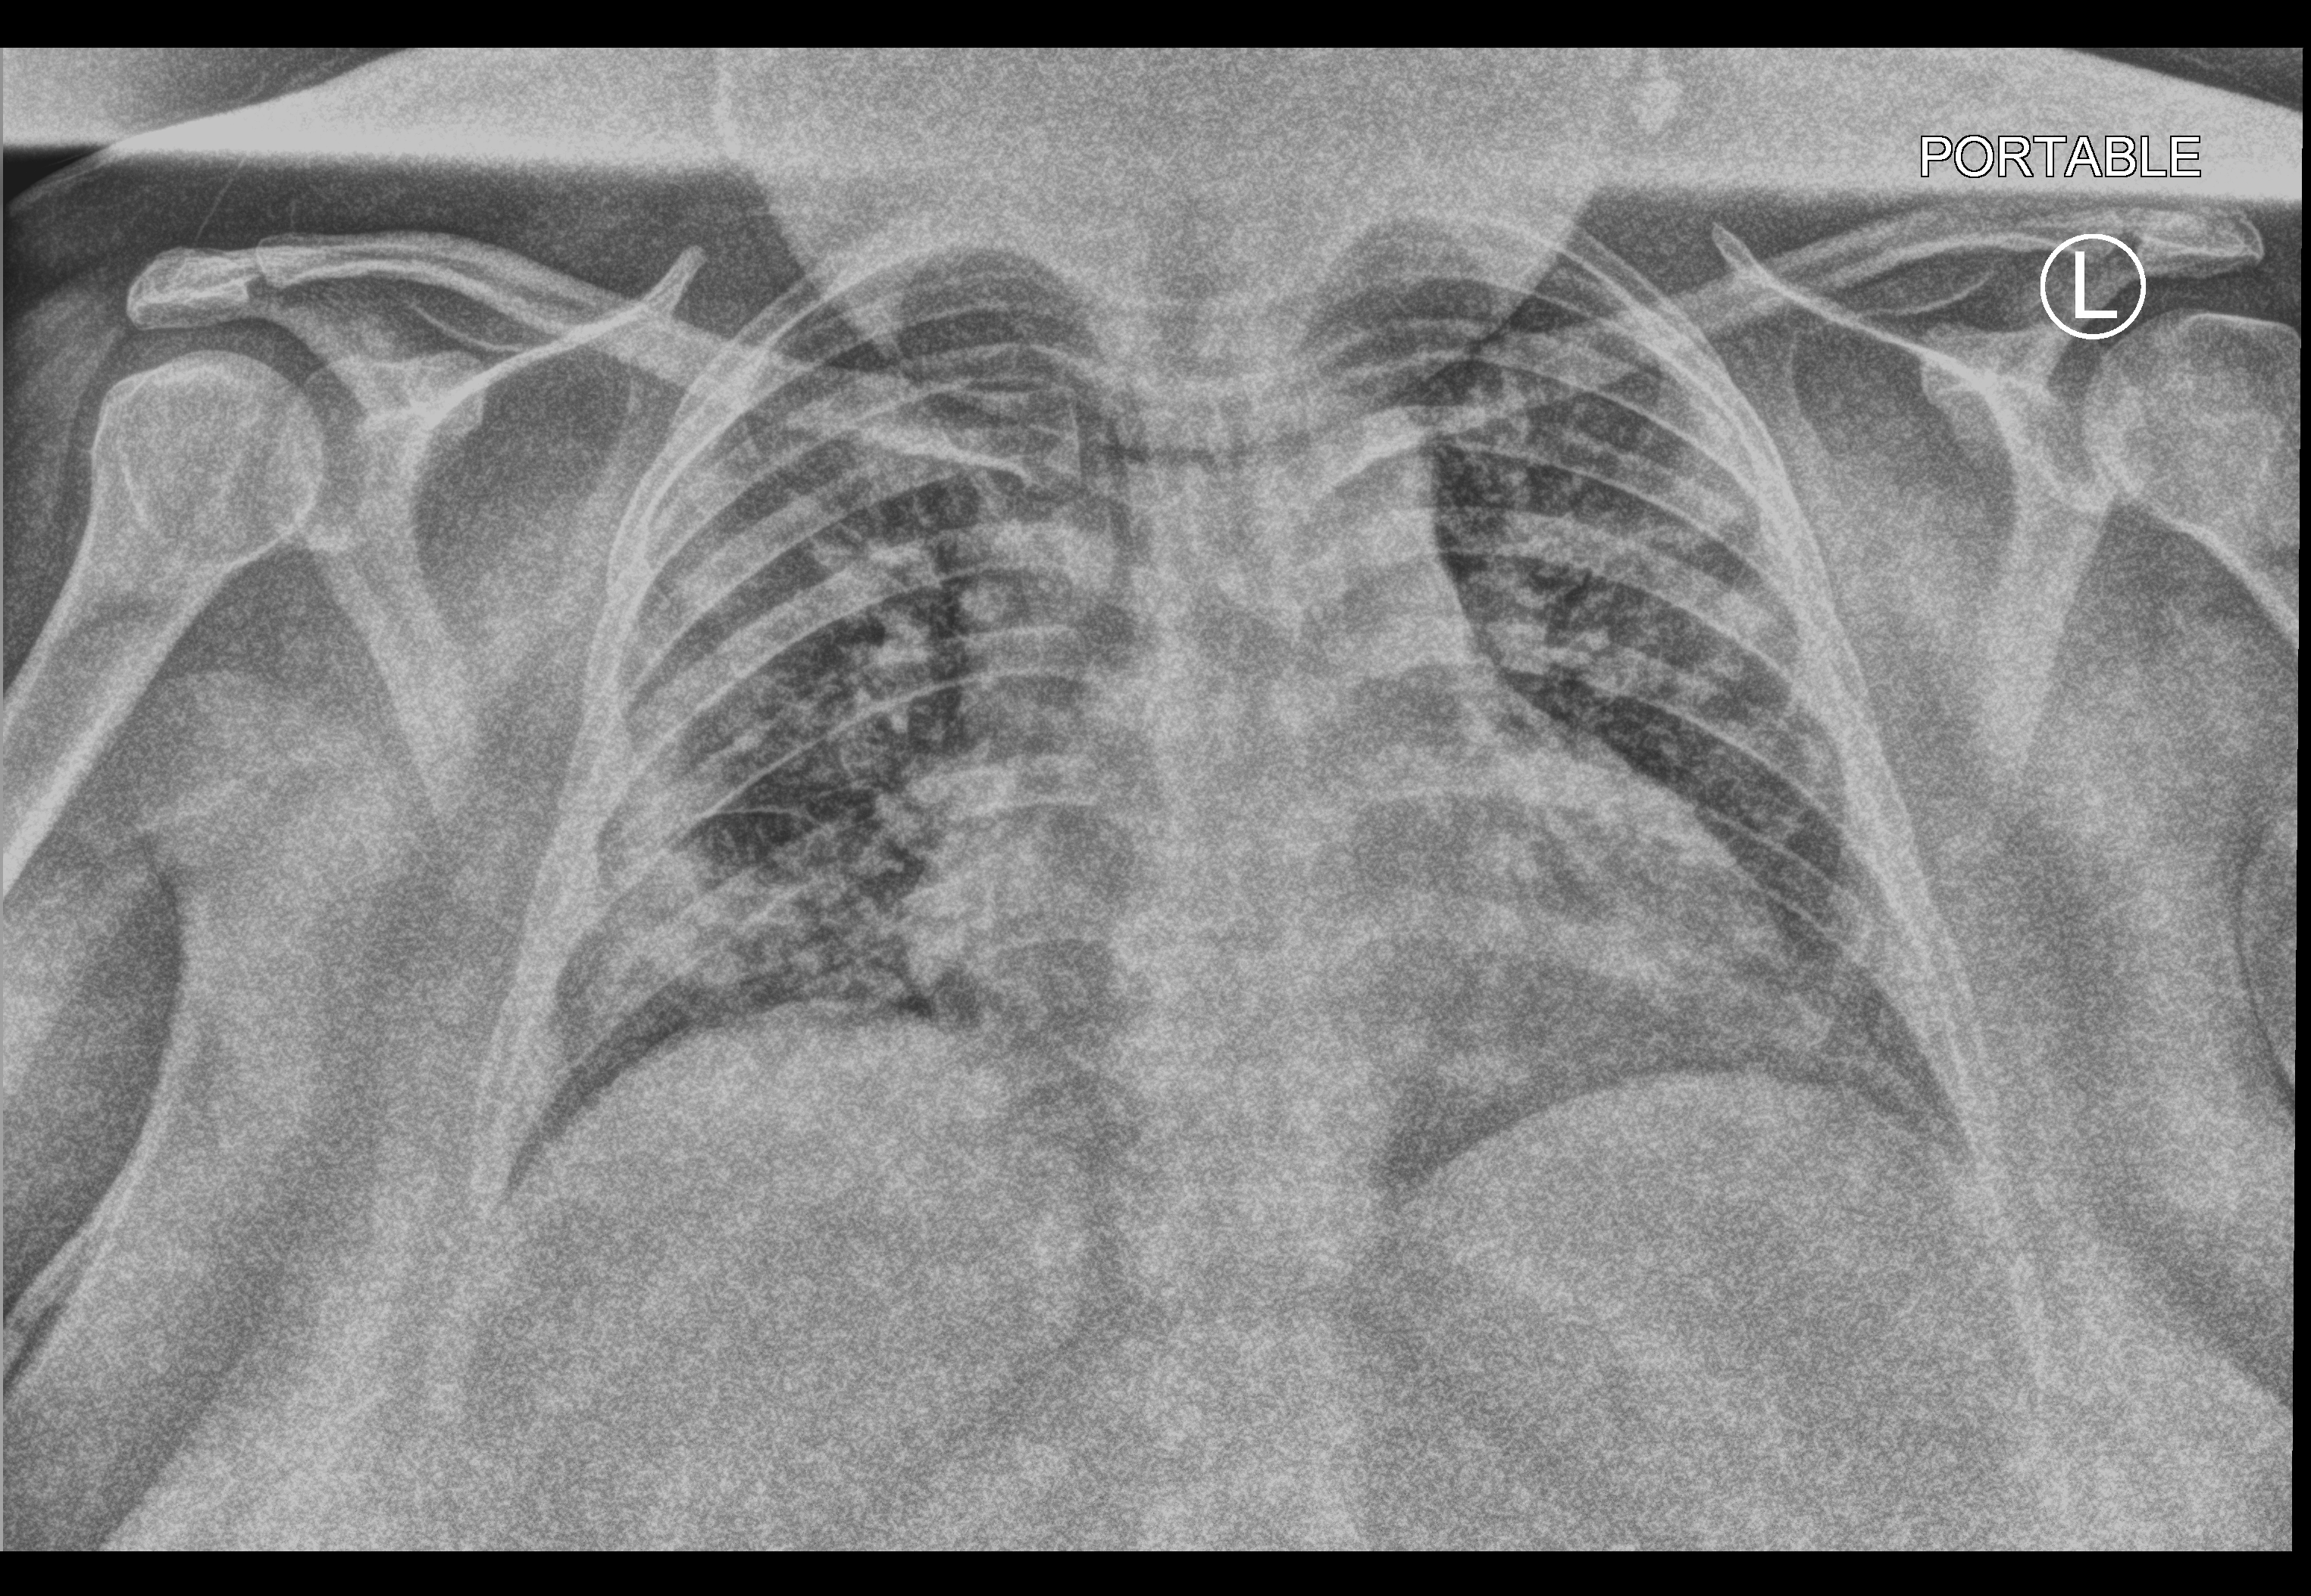
Portable chest radiograph; anteroposterior (AP) projection. Female patient hospitalised with COVID-19, age 18–59 years.
Admission-level facts for this patient (not findings on this image; timing relative to this image not recorded): COPD (admission record): no; mechanically ventilated during this hospital stay: yes; admitted to intensive care during this hospital stay: yes.